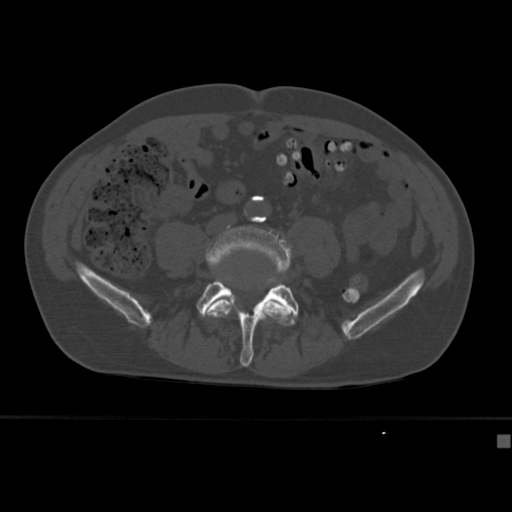
CT including the spine, one axial slice; position 95 of 430 along the scan axis; reconstruction kernel Br40s; bone window (W 1800 / L 400 HU); 1.5 mm slice thickness; 512 × 512 image matrix. Patient: male, 64 years. From the clinical record (not read from this slice): primary cancer: uterus; vertebrae with lytic lesions (as recorded): T1, T4, T5, T7, L5.
Structures marked on this image (semi-automatic segmentation, software-assisted and operator-edited):
- L4 vertebra: bounding box [x1, y1, x2, y2] px = [205, 224, 292, 325]
- L5 vertebra: [196, 280, 299, 367]